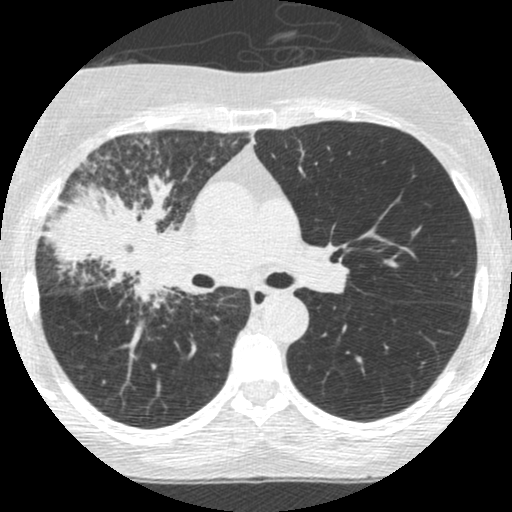
Low-dose screening chest CT, one axial slice; reconstruction kernel STANDARD; 120 kVp; lung window (W 1500 / L -600 HU); 512 × 512 image matrix.
Outlined on this slice (manually delineated by an expert):
- lesion 2 (tumor, hilum of right lung): box from (x=45, y=174) to (x=184, y=309) px